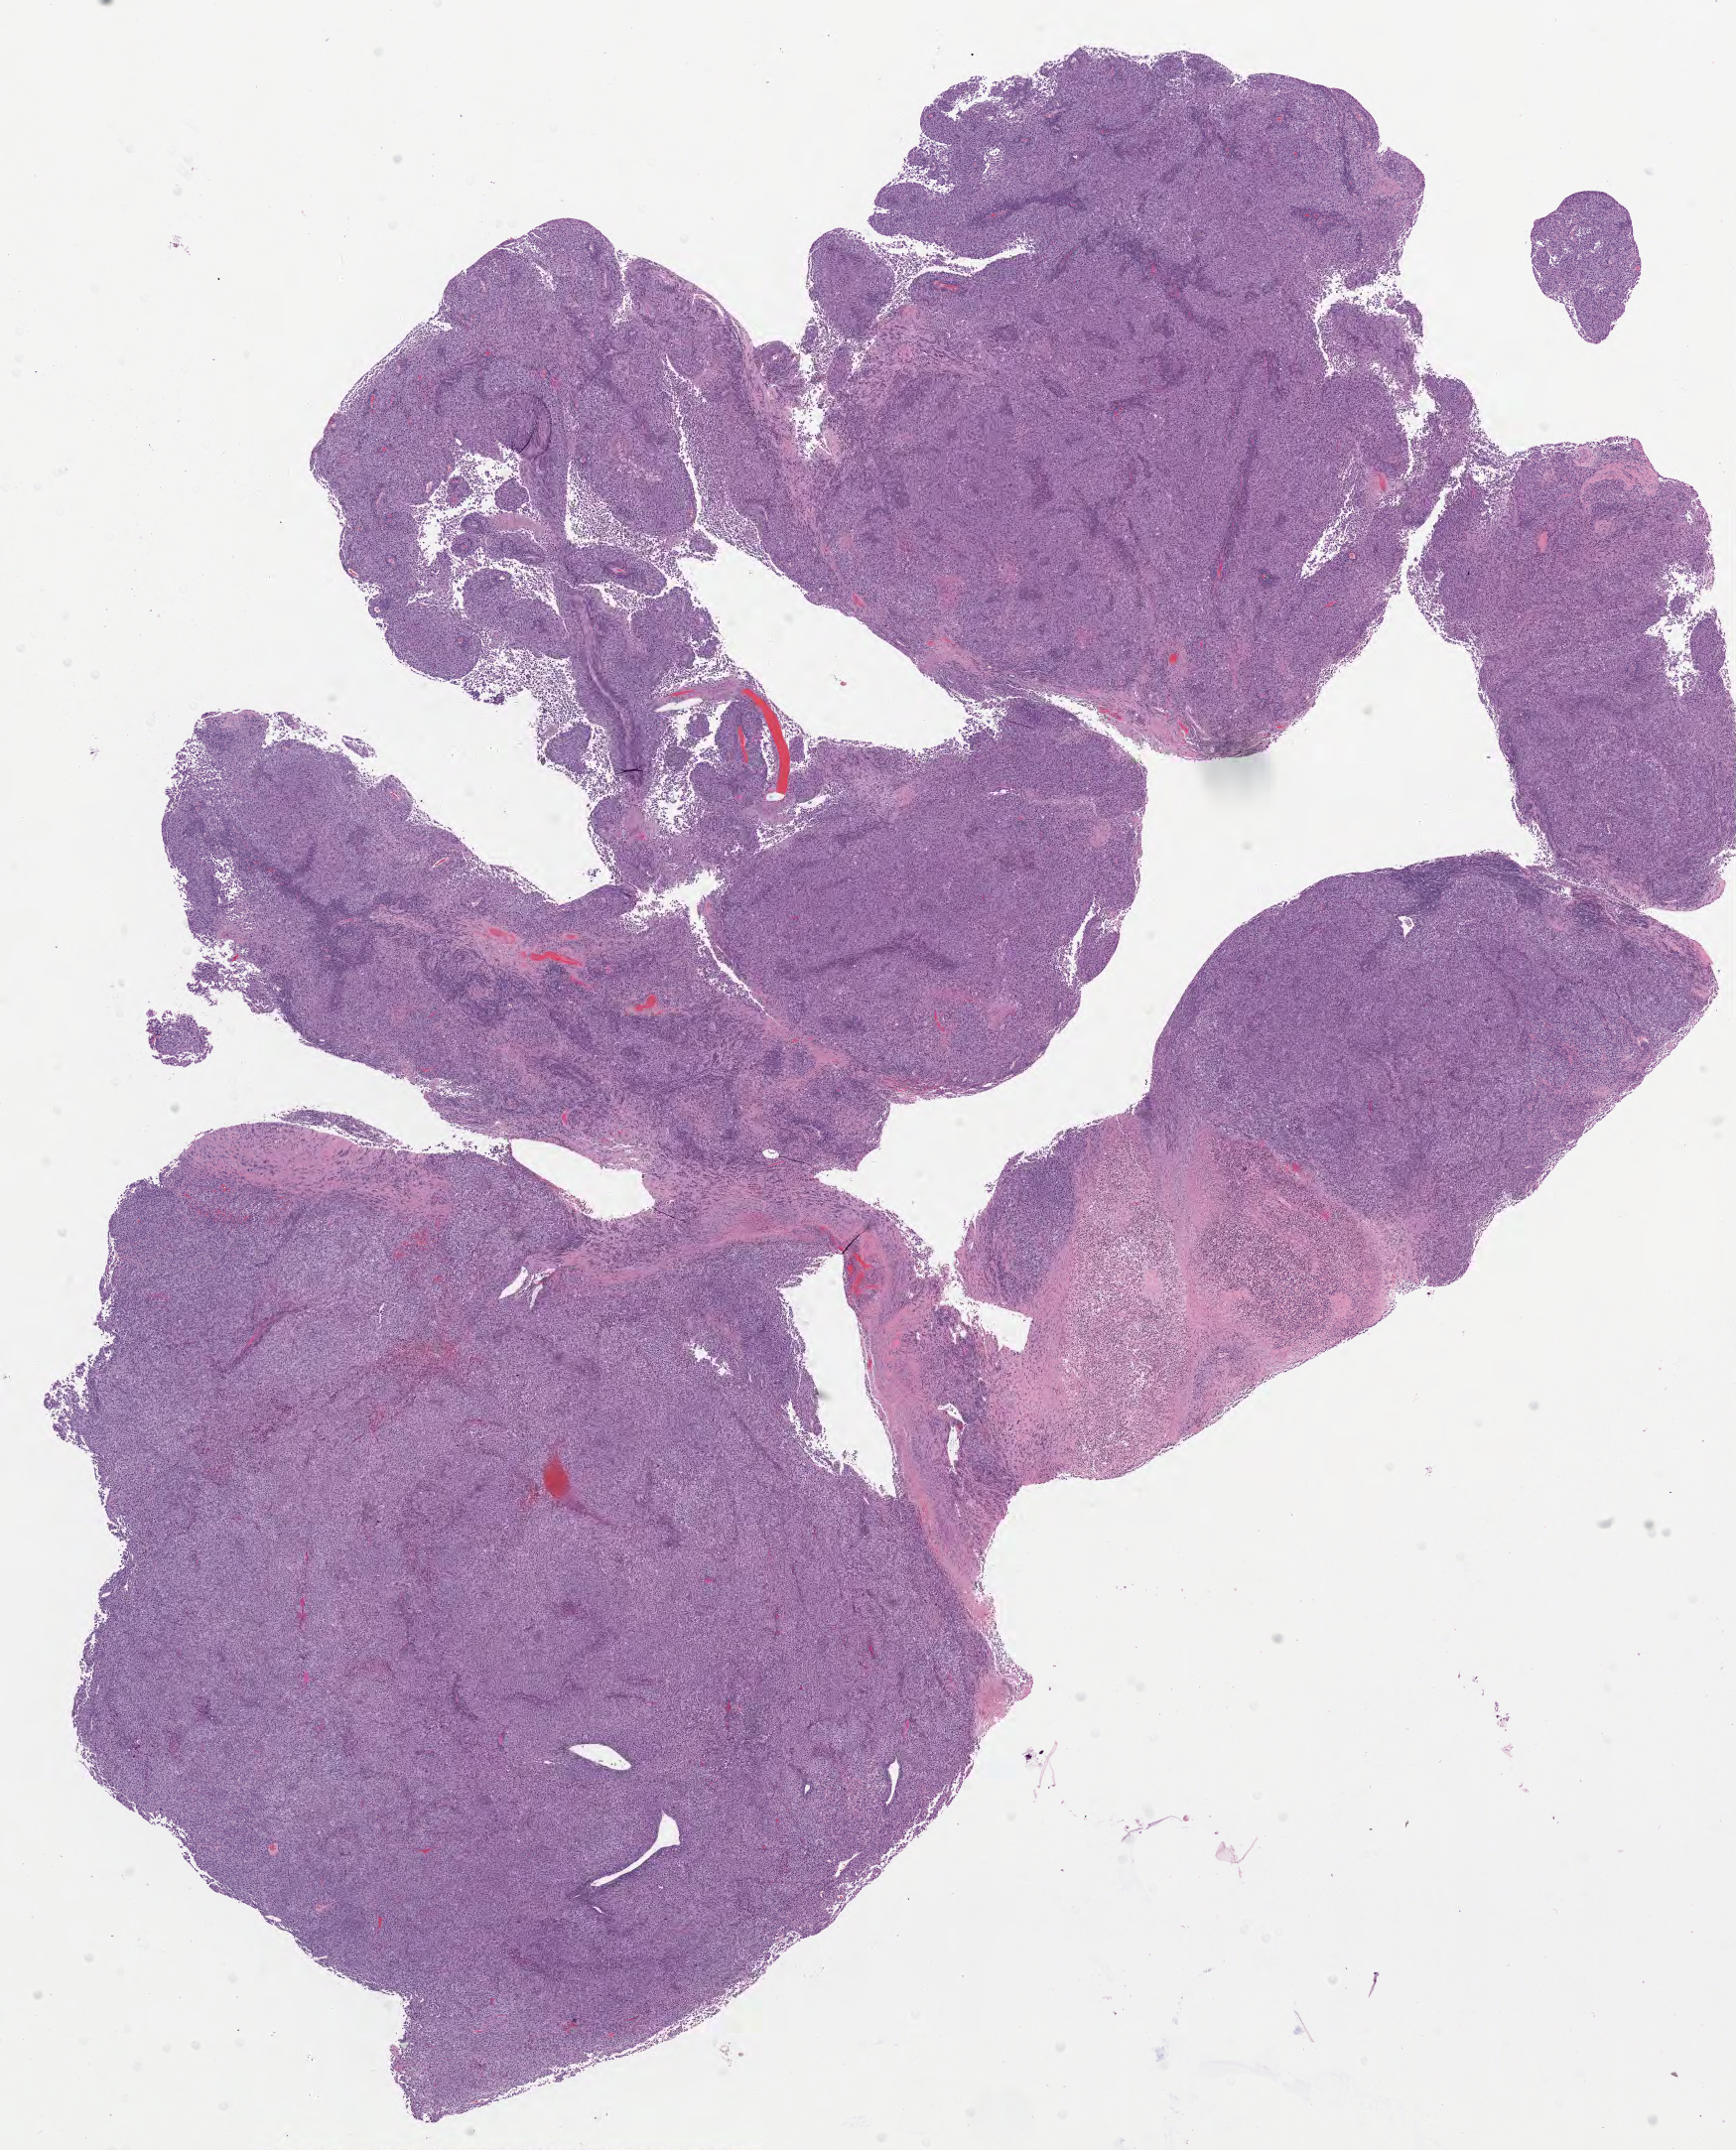
Whole-slide histology image, Hematoxylin and eosin (H&E) stained, shown as a low-resolution overview of the whole scanned area (about 14.0 x 17.3 mm, slide scanned at 20x); formalin-fixed paraffin-embedded (FFPE) diagnostic section; skin, primary tumour sample. Female patient; age at initial diagnosis 46 years.
* histologic diagnosis: Malignant melanoma, NOS